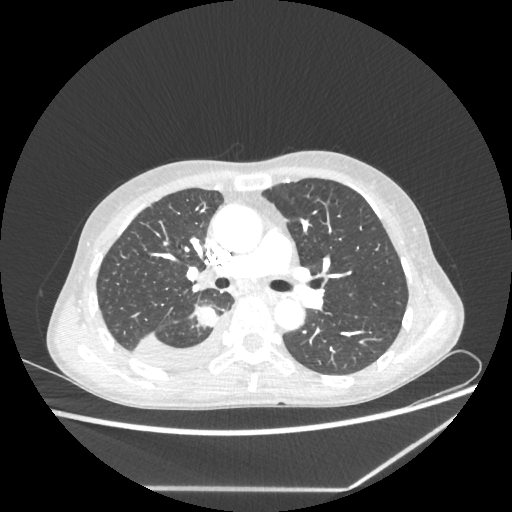
Chest CT, one axial slice; slice 141 of 237 in the series (ordered by position); reconstruction kernel STANDARD; lung window (W 1500 / L -600 HU); 1.25 mm slice thickness; 512 × 512 image matrix, field of view 364 × 364 mm. Patient: female, 59 years. Case-level facts recorded for this patient, not image findings: clinical TNM (as recorded): T1c N1 M1.
Structures marked on this image (bounding box drawn by a radiologist):
- lung tumour (recorded histology: adenocarcinoma): bounding box (x1, y1, x2, y2) in pixels: (192, 303, 218, 330)